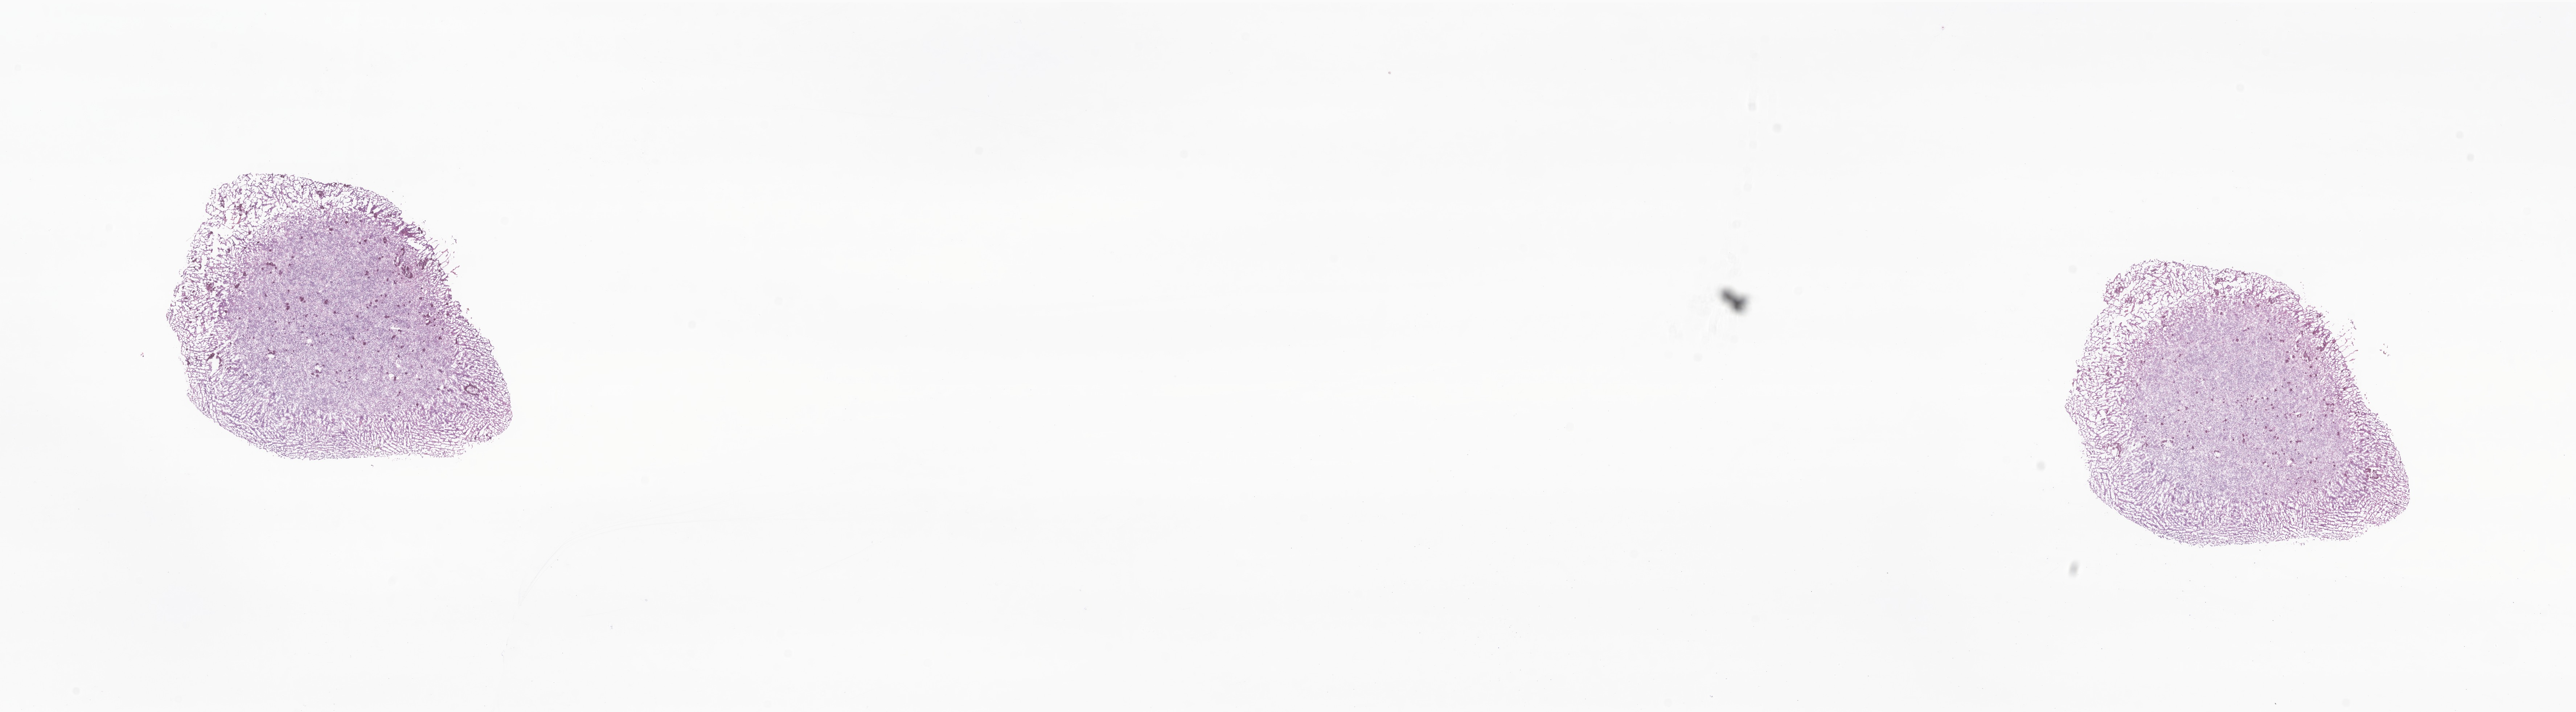
Whole-slide image, haematoxylin and eosin stain of tumor tissue from the brain — shown as a low-resolution overview of the whole scanned area (about 29.9 x 8.3 mm), frozen section (OCT-embedded). Patient: female, age 79 months (6 years 7 months).
Recorded diagnosis: Neoplasm, malignant.